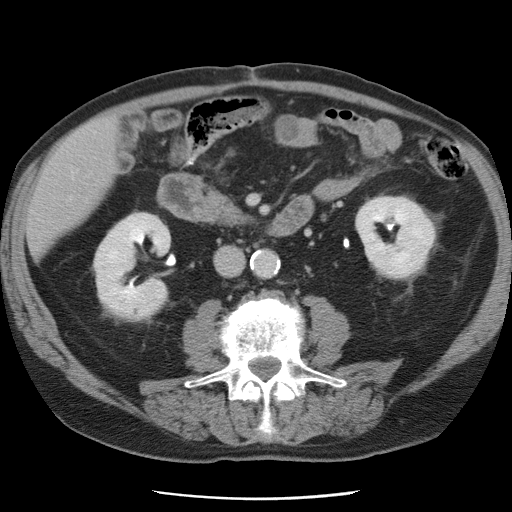
Contrast-enhanced abdominal CT, one axial slice; slice 20 of 78 in the series (ordered by position); intravenous contrast given; soft-tissue window (W 400 / L 40 HU); 512 × 512 image matrix, field of view 337 × 337 mm. Male patient, age 75 years. Case-level facts recorded for this patient, not image findings: diagnosis: colorectal cancer liver metastases, imaged before liver resection; multiple liver metastases: yes.
Annotated regions visible in this slice (outlined manually by an expert reader):
- liver: bounding box <29,118,116,256> (left, top, right, bottom; pixels)
- planned liver remnant (the part of the liver to remain after resection): <28,120,116,255>